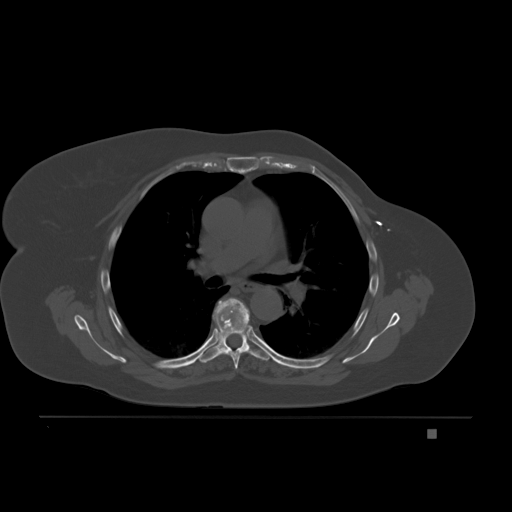
CT including the spine, one axial slice; slice 140 of 221 in the series (ordered by position); bone window (W 1800 / L 400 HU); 3 mm slice thickness; 512 × 512 image matrix, field of view 474 × 474 mm. Female patient, age 63 years. Case-level facts recorded for this patient, not image findings: primary cancer: breast.
Structures marked on this image (semi-automatic segmentation, software-assisted and operator-edited):
- T5 vertebra: bounding box <222,351,249,370> (left, top, right, bottom; pixels)
- T6 vertebra: <199,297,269,363>